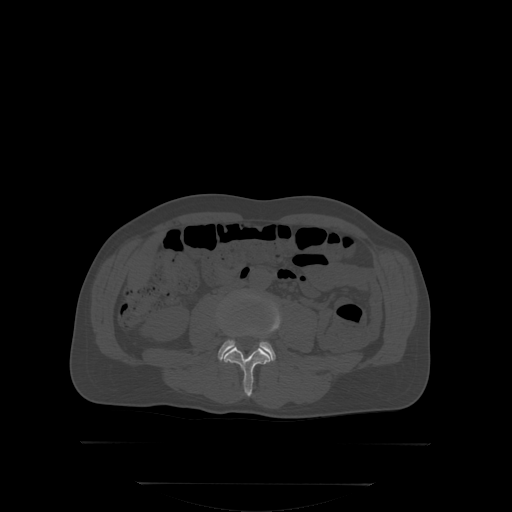
CT including the spine, one axial slice; slice 117 of 350 in the series (ordered by position); bone window (W 1800 / L 400 HU); 2.5 mm slice thickness; 512 × 512 image matrix, field of view 500 × 500 mm. Male patient, age 58 years. Case-level facts recorded for this patient, not image findings: primary cancer: prostate; vertebrae with lytic lesions (as recorded): L1.
Annotated regions visible in this slice (semi-automatic segmentation, software-assisted and operator-edited):
- L3 vertebra: bounding box <221,294,279,396> (left, top, right, bottom; pixels)
- L4 vertebra: <217,339,276,359>